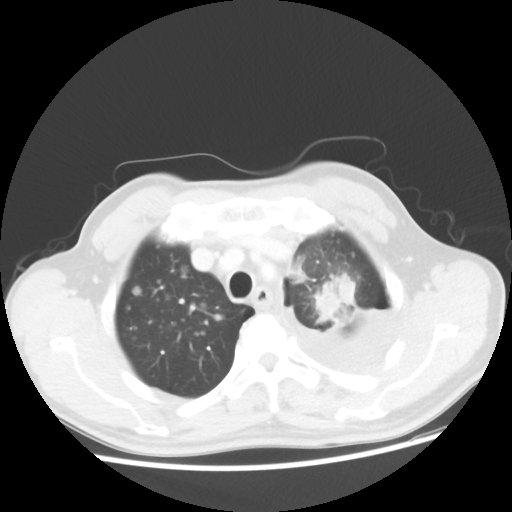
Chest CT, one axial slice. Lung window (W 1500 / L -600 HU). 5 mm slice thickness. 512 × 512 image matrix, field of view 362 × 362 mm. Male patient, age 55 years. From the clinical record (not read from this slice): clinical TNM (as recorded): T2 N3 M1a; histopathological grade: G3.
Outlined on this slice (bounding box drawn by a radiologist):
- lung tumour (recorded histology: squamous cell carcinoma): bounding box [x1, y1, x2, y2] px = [309, 265, 357, 330]